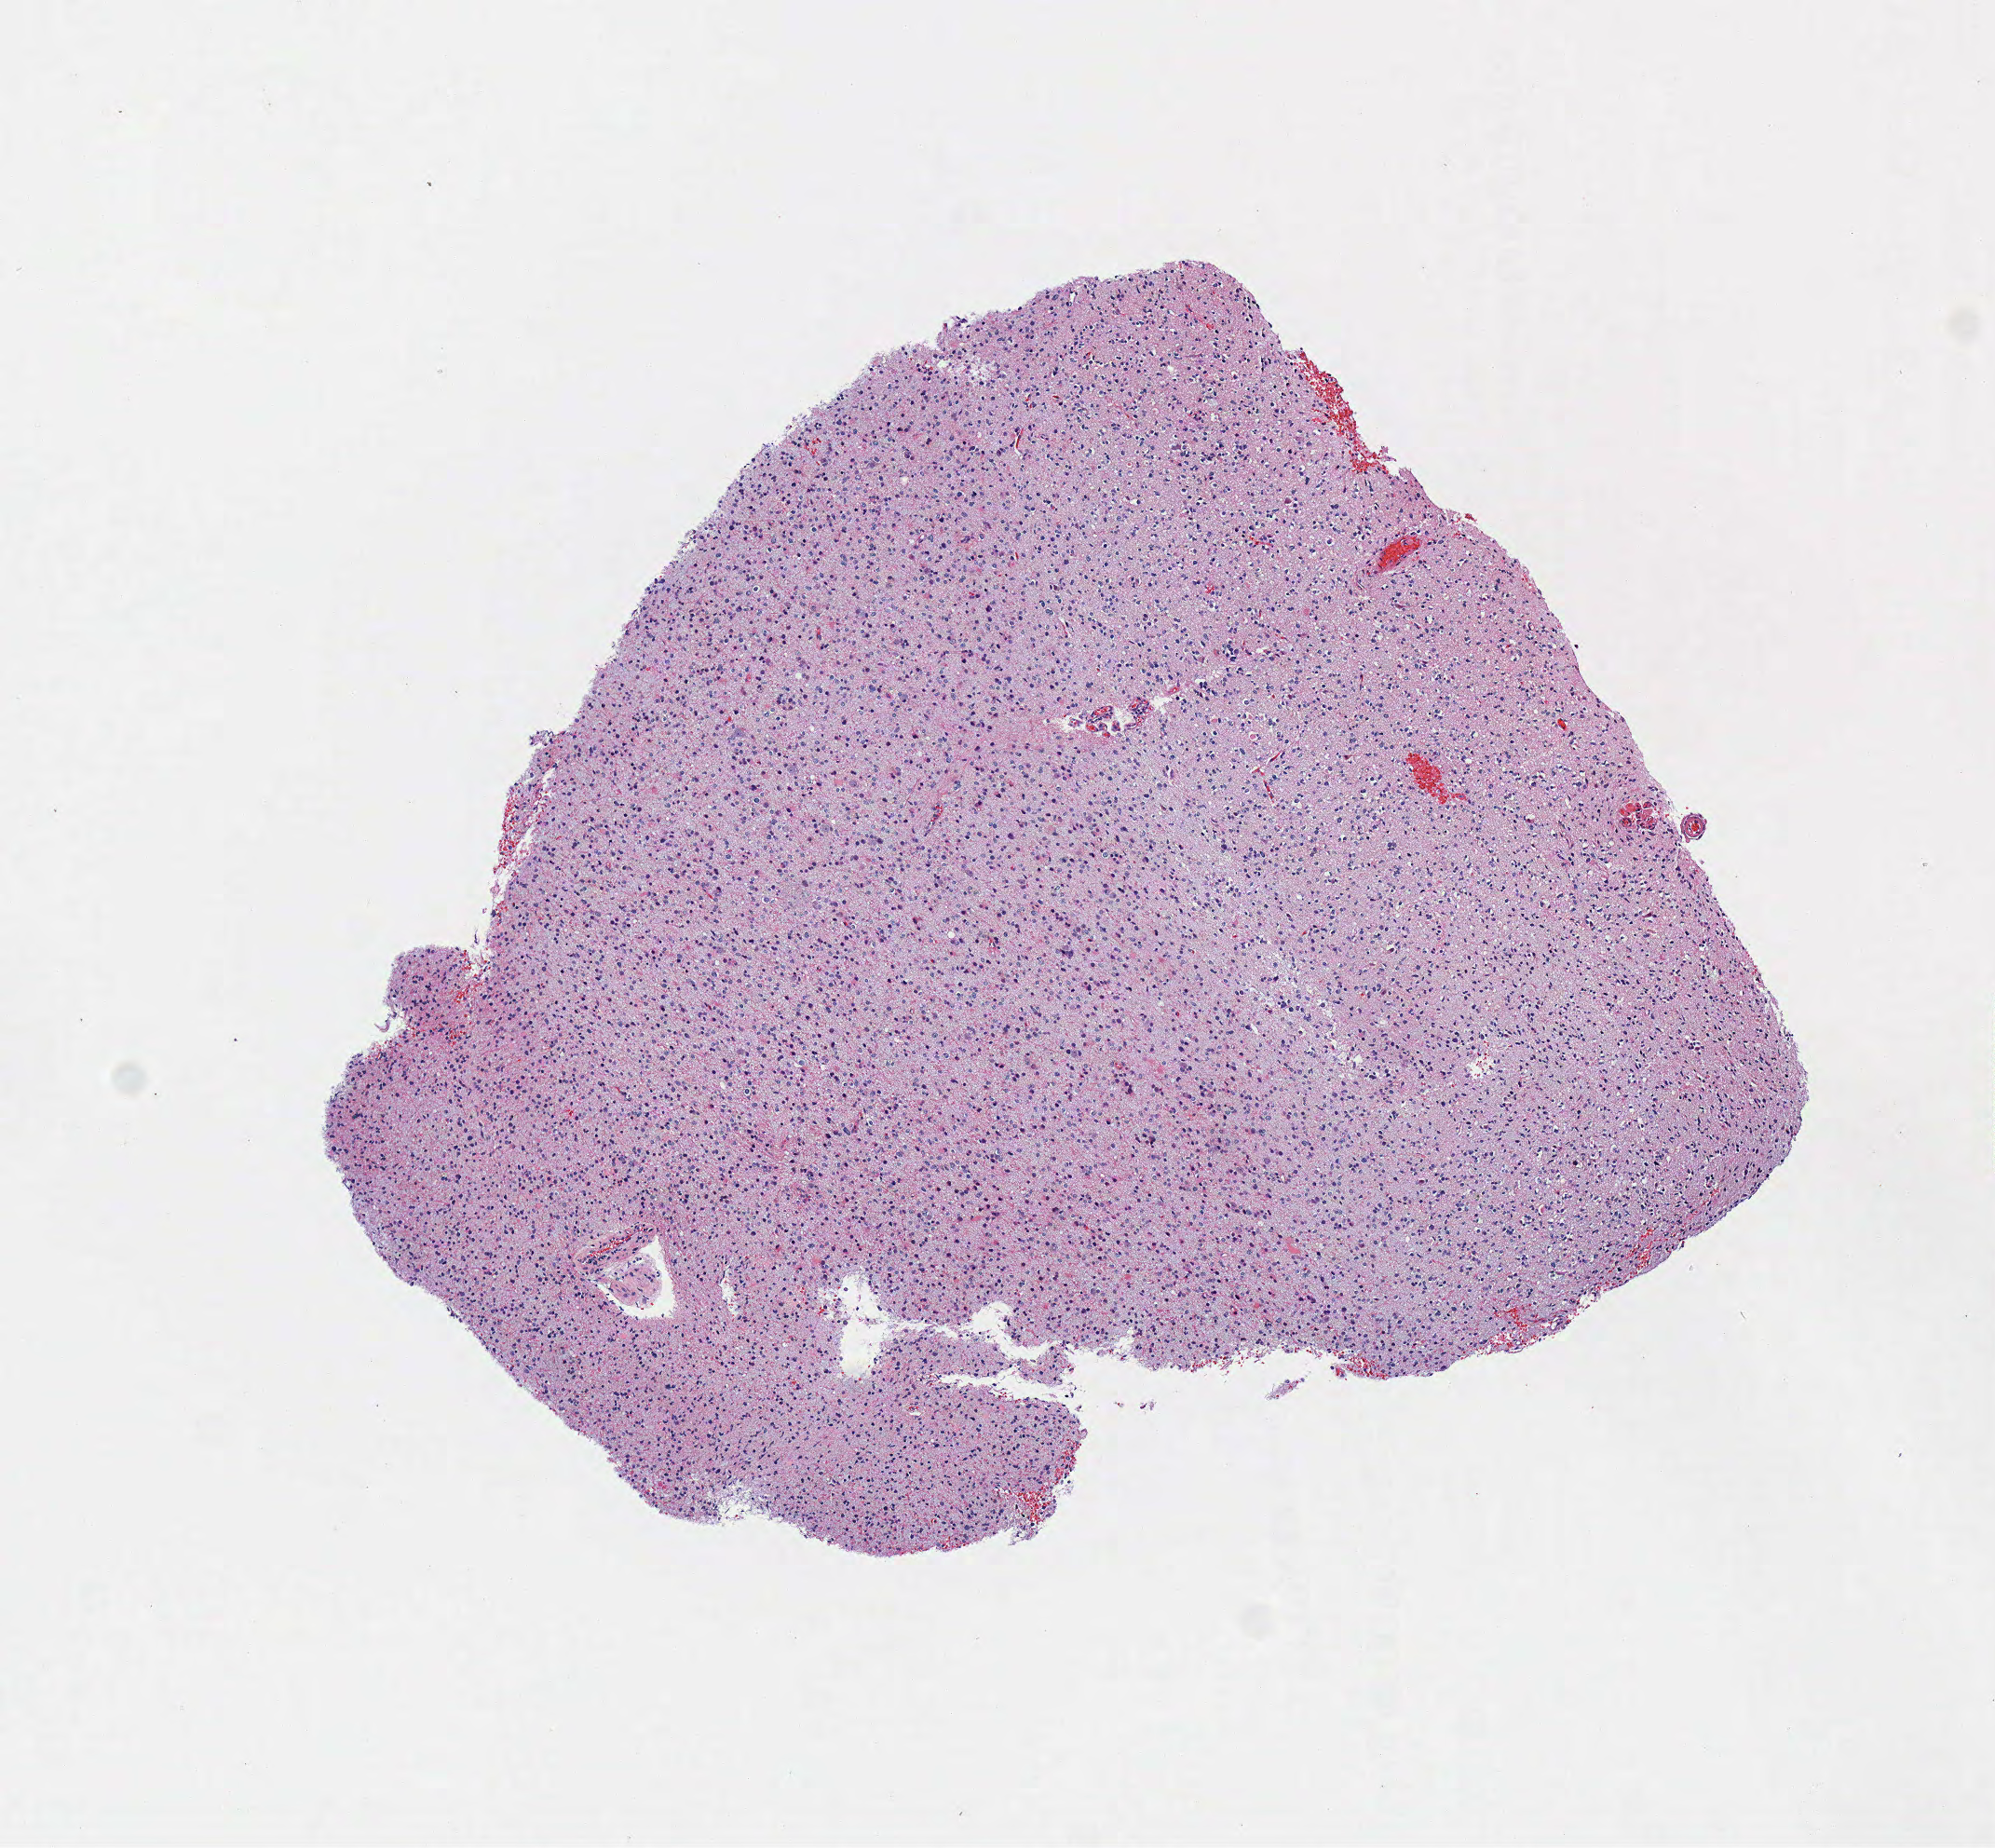
Hematoxylin and eosin (H&E) stained whole-slide image, low-resolution overview of the scanned area, about 4.2 x 3.9 mm; frozen section from the top of the tissue portion; brain, primary tumour sample. Patient: male, age at initial diagnosis 29 years. Histologic grade: G2 (moderately differentiated). Slide review estimates, as recorded: tumour cells 100%, tumour nuclei 75%, normal cells 0%, stromal cells 0%, necrosis 0%.
• diagnosis: Mixed glioma